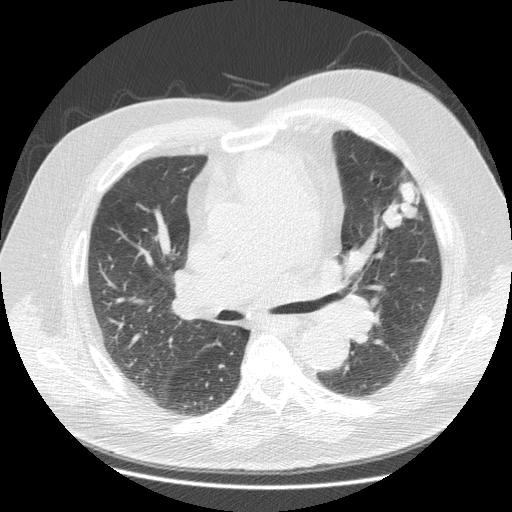
Low-dose screening chest CT, axial slice. Second annual screen. Lung window (W 1500 / L -600 HU). Standard (soft-tissue) reconstruction kernel (STANDARD). Slice 63 of 116 in the series. Male, age 67 years at enrolment. Former smoker at enrolment.
• Expert reader's lesion annotation, bounding box [x1, y1, x2, y2] px = [369, 168, 435, 235].
• The screening reader recorded 3 non-calcified nodules or masses ≥4 mm on this exam (left upper lobe, left upper lobe, left upper lobe); which of them this box marks is not recorded.
• Participant outcome: lung cancer diagnosed 34 days after this screen — small cell carcinoma, NOS, left upper lobe, undifferentiated (G4), stage IV (AJCC 6th edition), 17 mm at pathology.